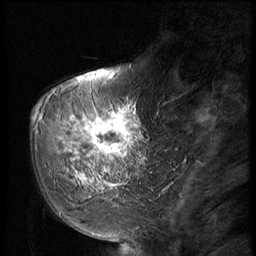
Breast MRI (dynamic contrast-enhanced), one sagittal slice. Position 18 of 56 along the scan axis. Dynamic contrast-enhanced series, image 2 of 2 at this slice position (ordered by acquisition). 1.5 T. TE 4.2 ms, TR 9 ms. 2.5 mm slice thickness. 256 × 256 image matrix, field of view 180 × 180 mm. Female patient, age 51 years. From the clinical record (not read from this slice): setting: breast cancer imaged before/during neoadjuvant chemotherapy; receptor status: triple-negative.
Structures marked on this image (semi-automatic segmentation, software-assisted and operator-edited):
- analysis volume of interest (the breast-tissue region the enhancement analysis was run in; not a lesion): bounding box (x1, y1, x2, y2) in pixels: (60, 98, 147, 197)
- tumour enhancement mask (voxels above the 140 % enhancement threshold inside the analysis volume of interest): (70, 102, 137, 189)